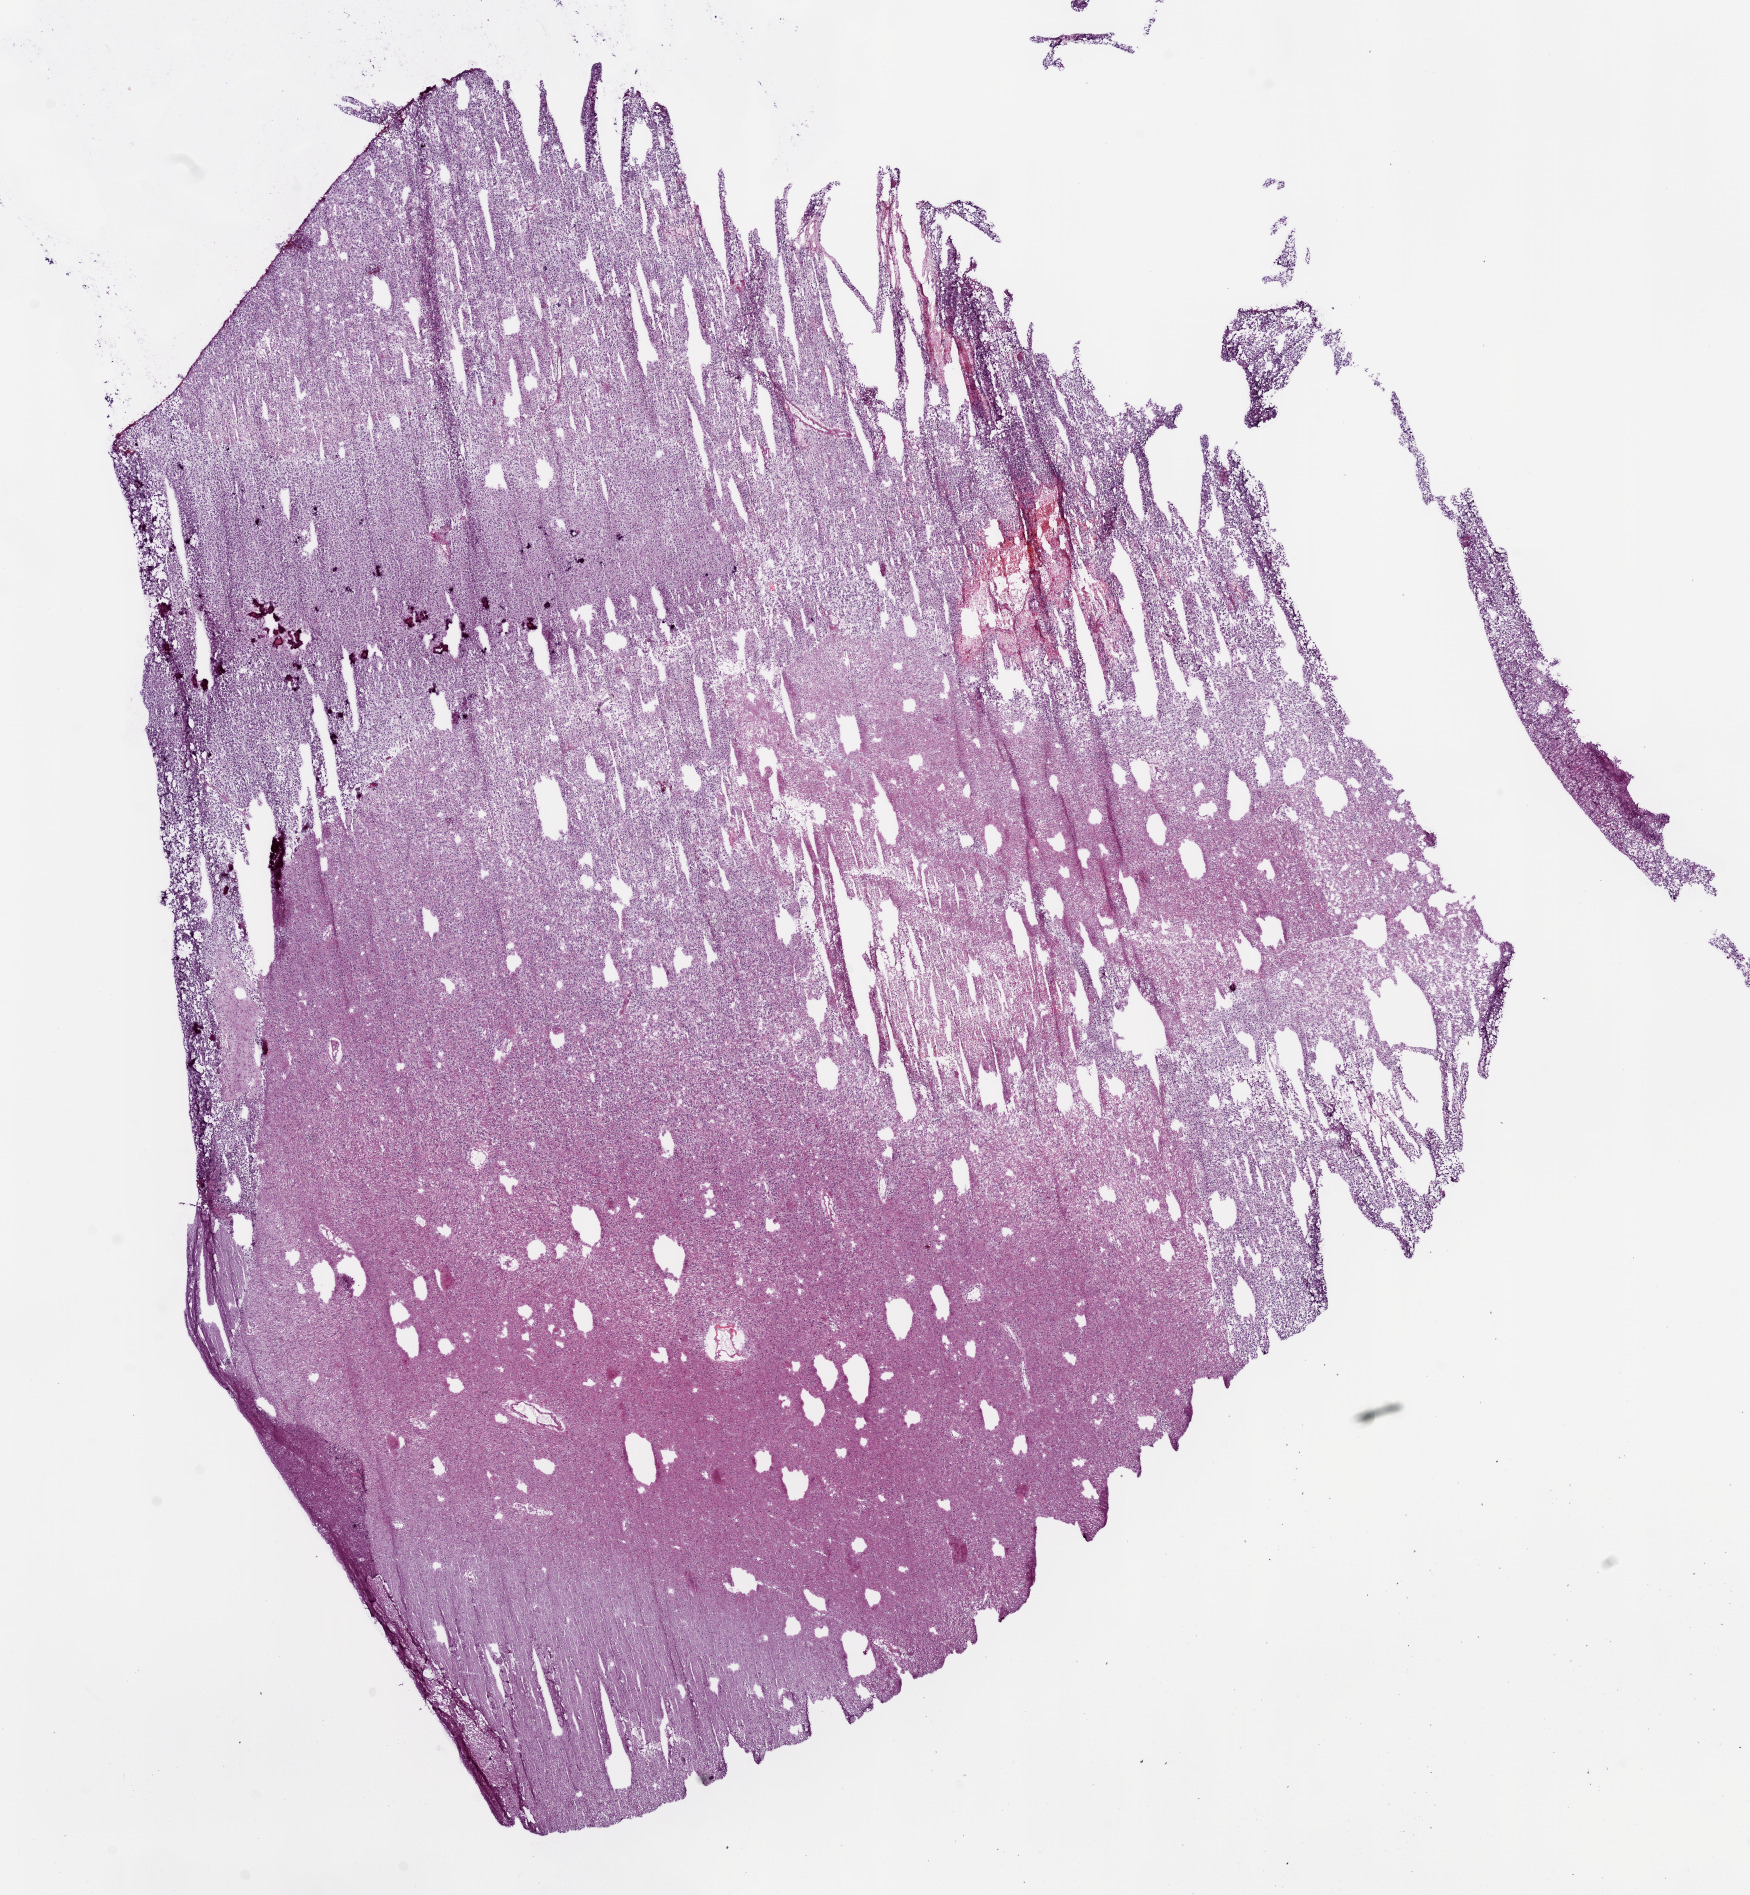
Whole-slide histology image, H&E — shown as a low-resolution overview of the whole scanned area (about 14.0 x 15.2 mm), frozen section from the bottom of the tissue portion, brain, primary tumour sample. Female, age 37 years at initial diagnosis. Histologic grade: G3 (poorly differentiated). Slide review estimates, as recorded: tumour cells 100%, tumour nuclei 80%, normal cells 0%, stromal cells 0%, necrosis 0%.
Histologic diagnosis: Mixed glioma. Laterality: left.